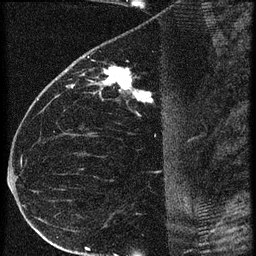
Breast MRI (dynamic contrast-enhanced), one sagittal slice. Position 33 of 60 along the scan axis. 3 images stored at this slice position (order not interpretable as contrast timing). 1.5 T. TE 4.2 ms, TR 20.4 ms. 1.5 mm slice thickness. 256 × 256 image matrix, field of view 180 × 180 mm. Patient: female, 35 years. From the clinical record (not read from this slice): setting: breast cancer imaged before/during neoadjuvant chemotherapy; receptor status: HR-positive, HER2-negative.
Annotated regions visible in this slice (semi-automatically segmented with operator editing):
- analysis volume of interest (the breast-tissue region the enhancement analysis was run in; not a lesion): bounding box (x1, y1, x2, y2) in pixels: (65, 60, 169, 119)
- tumour enhancement mask (voxels above the 90 % enhancement threshold inside the analysis volume of interest): (68, 68, 152, 103)